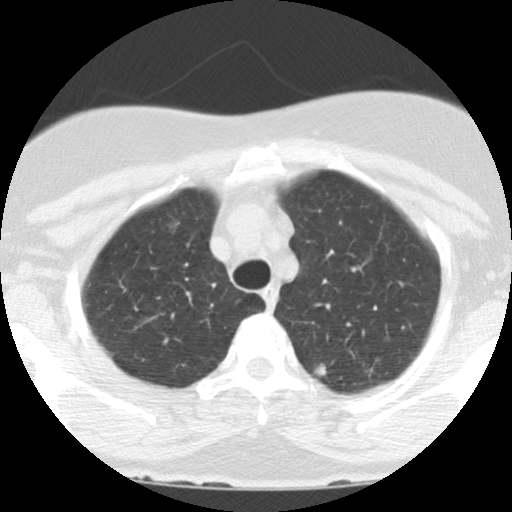
Low-dose screening chest CT, one axial slice; slice 104 of 123 in the series (ordered by position); reconstruction kernel STANDARD; lung window (W 1500 / L -600 HU); 512 × 512 image matrix, field of view 290 × 290 mm.
Outlined on this slice (outlined manually by an expert reader):
- lesion 1 (tumor, upper lobe of left lung): bounding box [x1, y1, x2, y2] px = [314, 363, 327, 377]